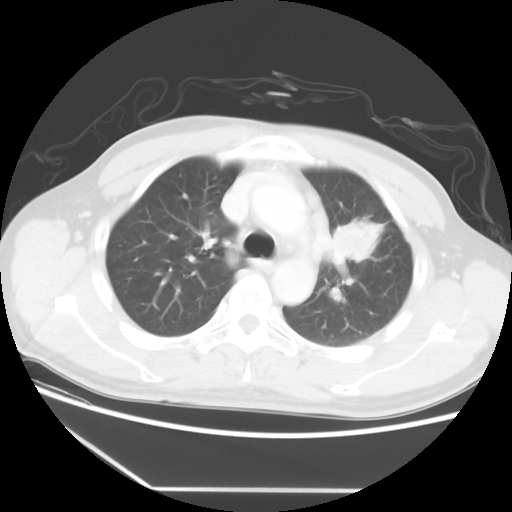
Chest CT, one axial slice; position 40 of 56 along the scan axis; 120 kVp; lung window (W 1500 / L -600 HU); 512 × 512 image matrix, field of view 373 × 373 mm. Male patient, age 53 years. From the clinical record (not read from this slice): clinical TNM (as recorded): T2a N1 M1b.
Structures marked on this image (rectangle marked by the reading radiologist):
- lung tumour (recorded histology: adenocarcinoma): bounding box [x1, y1, x2, y2] px = [331, 217, 384, 273]